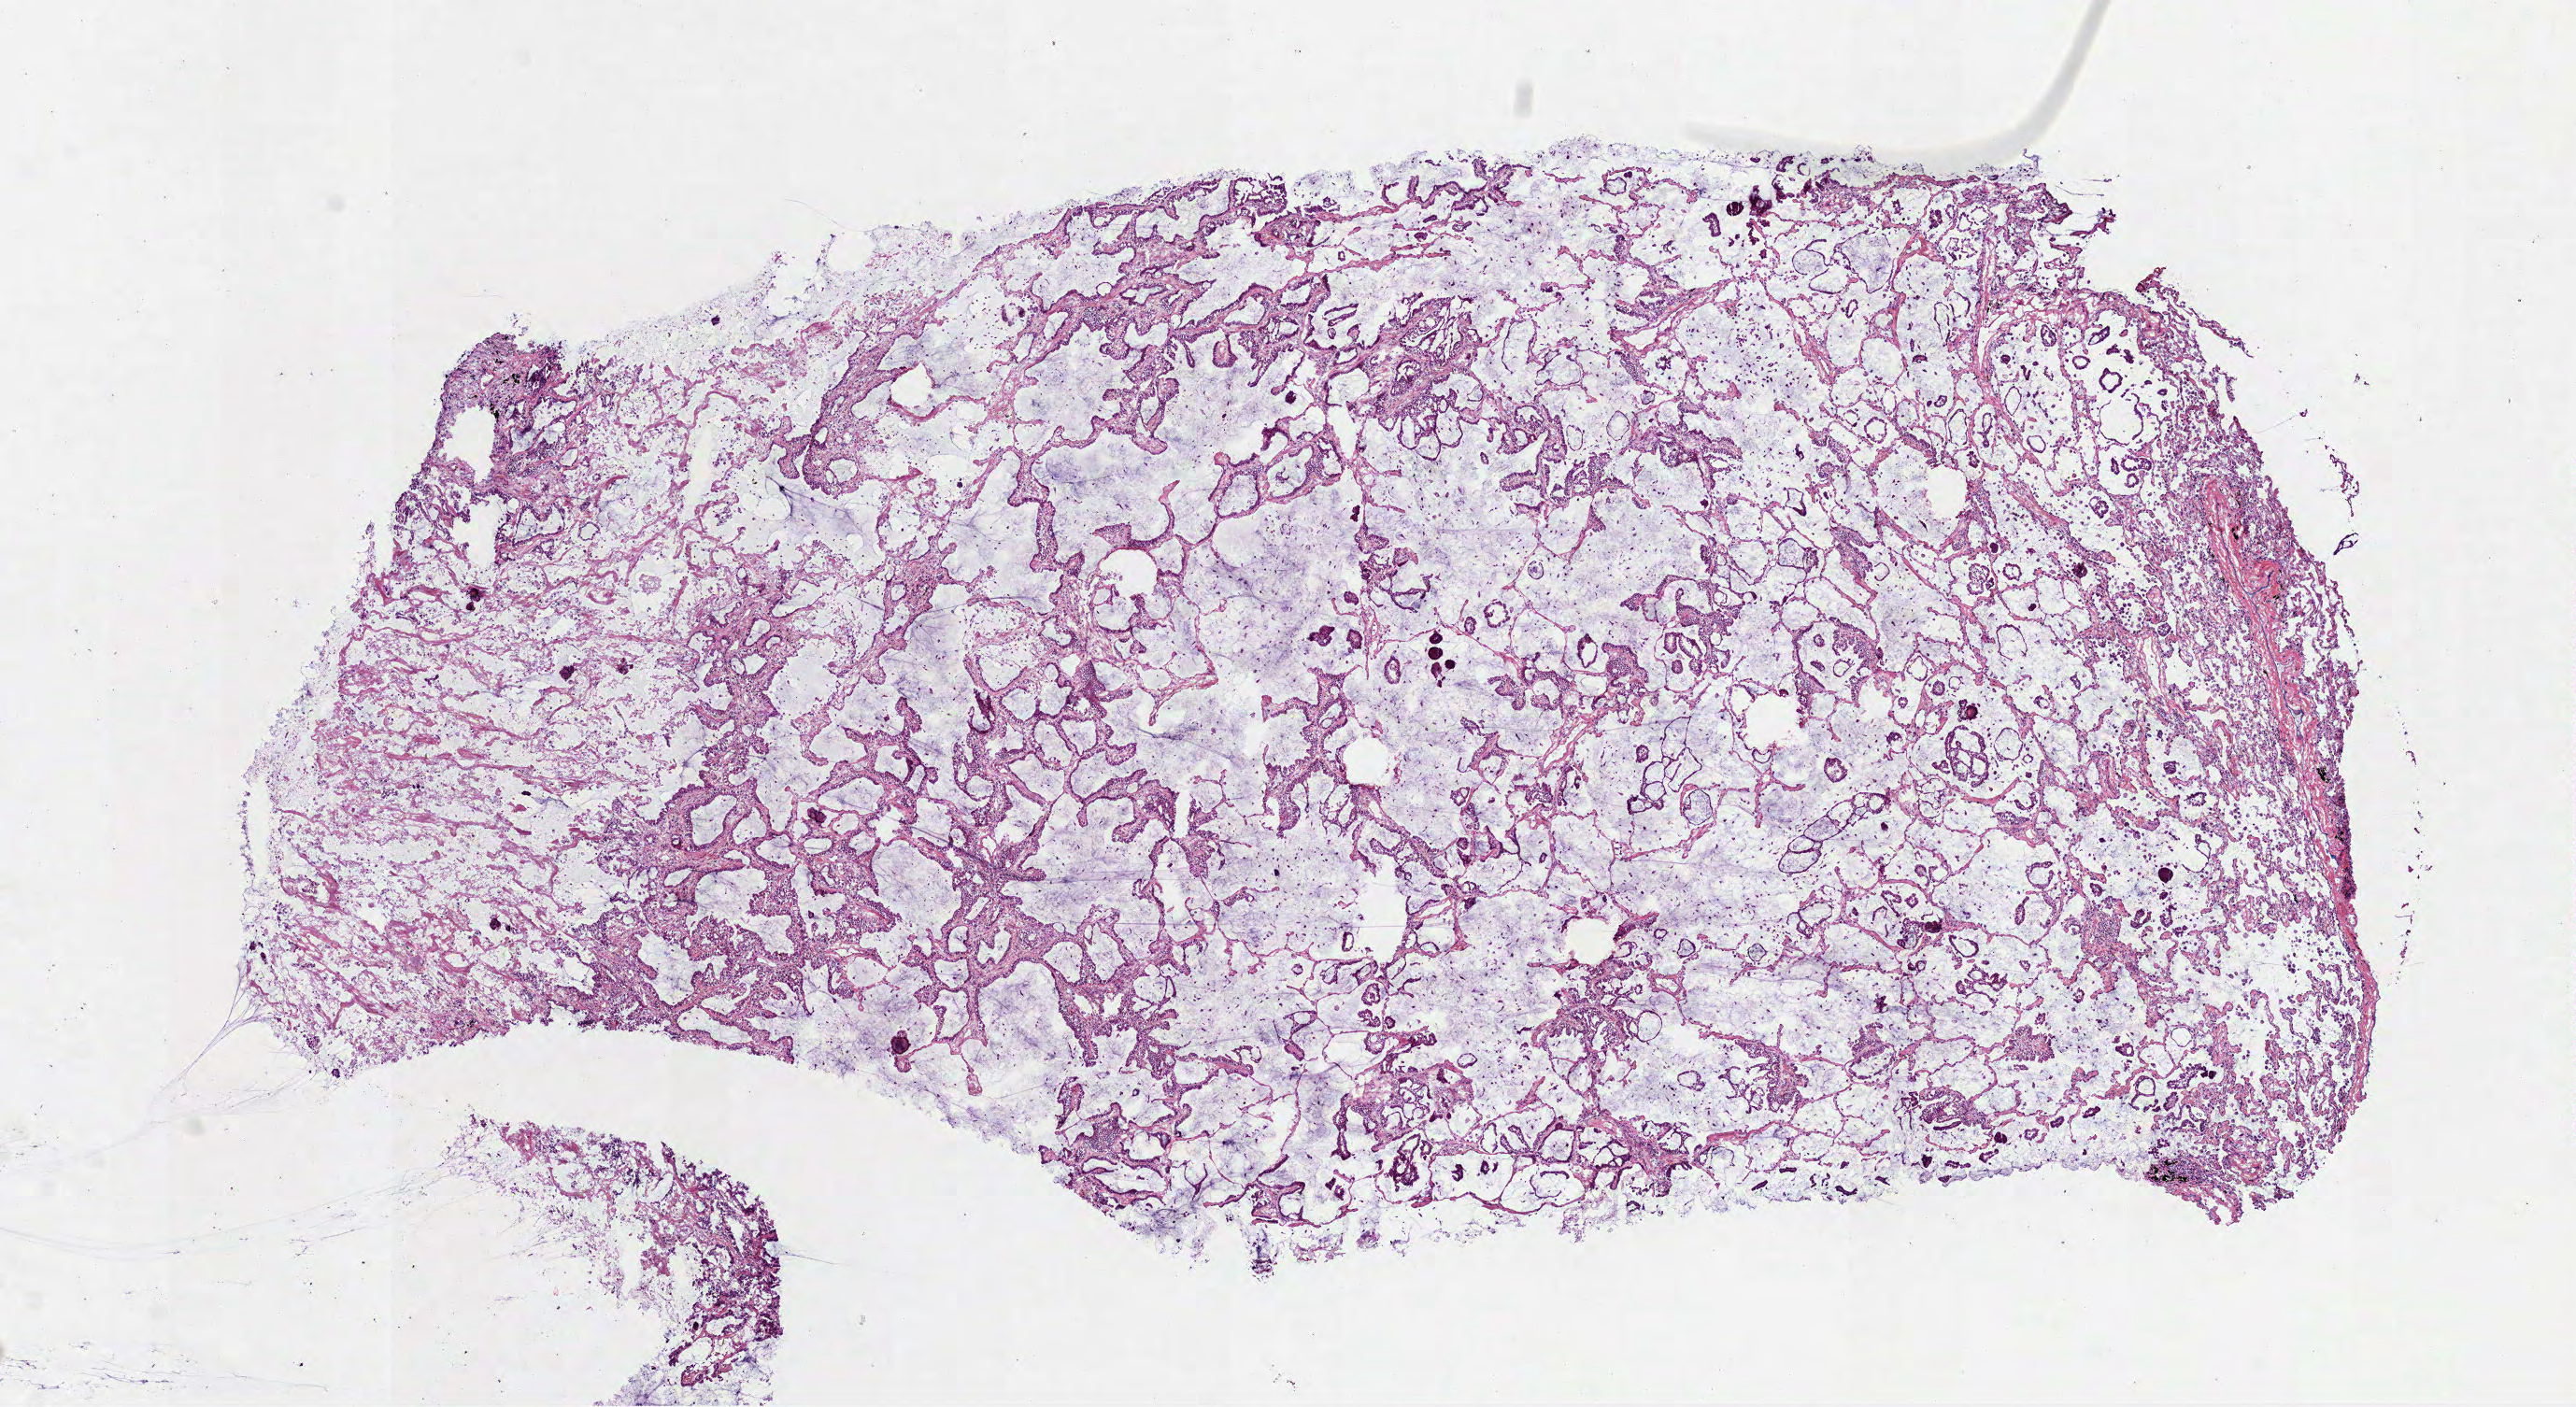
Whole-slide histology image, H&E-stained — a low-resolution overview of the entire scanned area, about 11.1 x 6.1 mm, frozen section from the bottom of the tissue portion, primary tumour sample from the lung. Patient: female, age at initial diagnosis 60 years. Slide review estimates, as recorded: tumour cells 82%, tumour nuclei 80%.
Pathologic diagnosis: Bronchio-alveolar carcinoma, mucinous (upper lobe, lung).